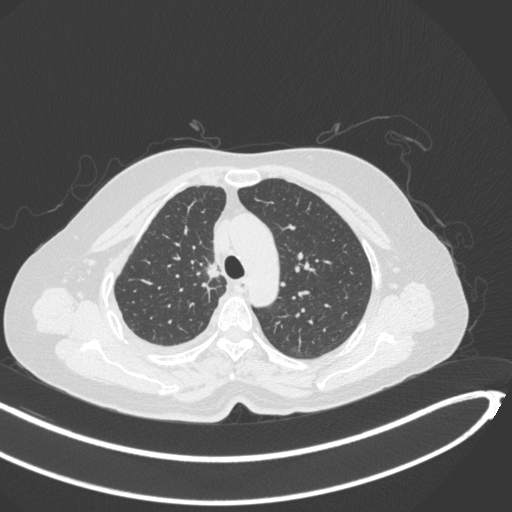
Chest CT, one axial slice; position 227 of 297 along the scan axis; reconstruction kernel B31f; 120 kVp; lung window (W 1500 / L -600 HU); 1 mm slice thickness; 512 × 512 image matrix, field of view 400 × 400 mm. Patient: female, 64 years. From the clinical record (not read from this slice): clinical TNM (as recorded): T1b N0 M1.
Structures marked on this image (rectangle marked by the reading radiologist):
- lung tumour (recorded histology: adenocarcinoma): bounding box <201,259,220,282> (left, top, right, bottom; pixels)